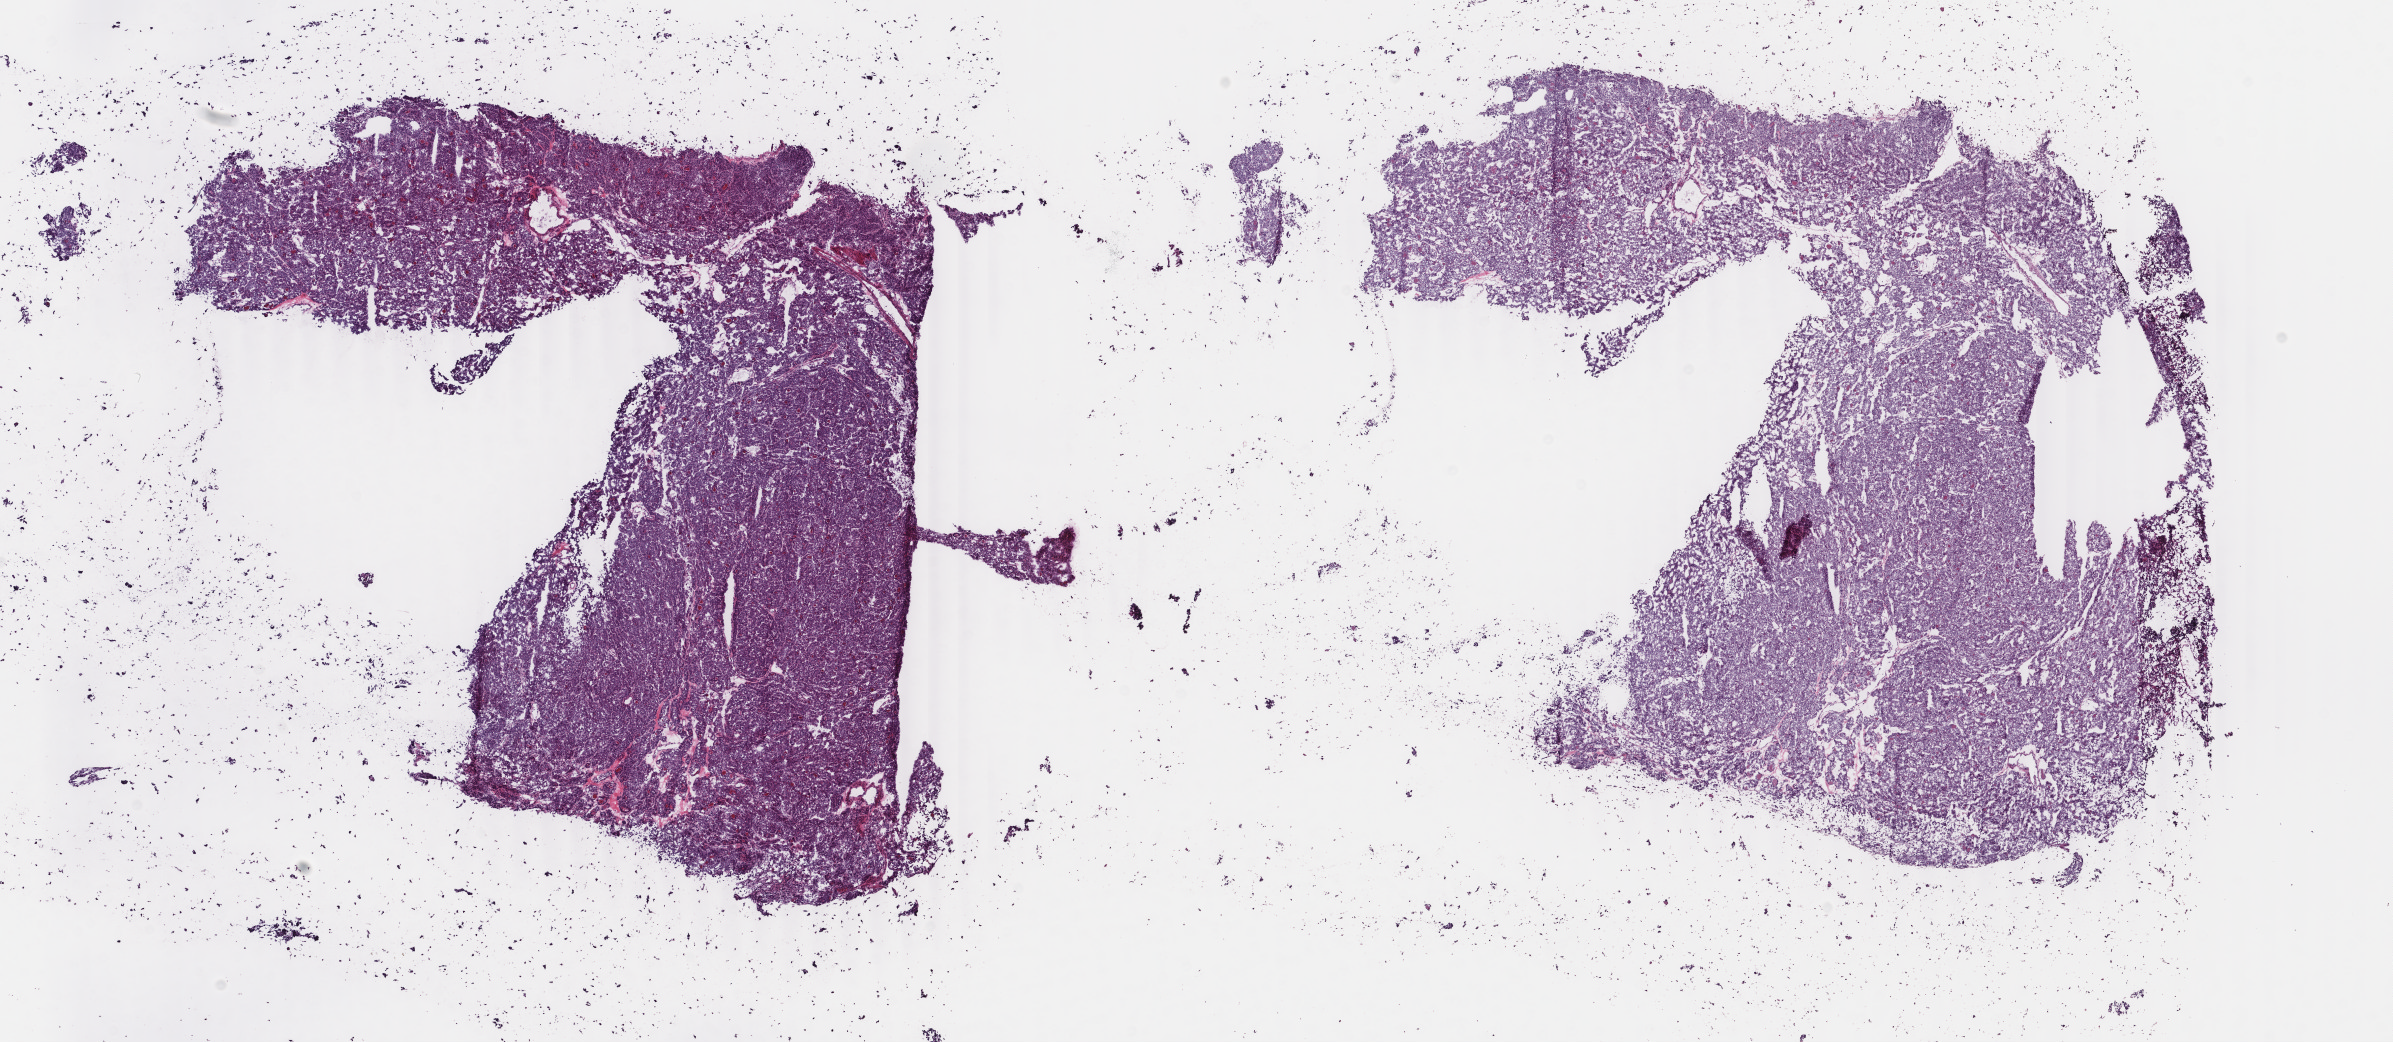
H&E whole-slide image, low-resolution overview of the scanned area, about 19.0 x 8.3 mm (slide scanned at 40x); frozen section from the top of the tissue portion; sample: primary tumour, thyroid. Patient: female, age at initial diagnosis 19 years. Pathologist review of this section (percent, as recorded): tumour cells 100%, tumour nuclei 98%, normal cells 0%, stromal cells 0%, necrosis 0%. Infiltration values recorded for this section: lymphocyte infiltration 0%, monocyte infiltration 0%, neutrophil infiltration 0%.
* histologic diagnosis: Papillary carcinoma, follicular variant (thyroid gland)
* TNM: T1b N0 M0
* AJCC pathologic stage: I